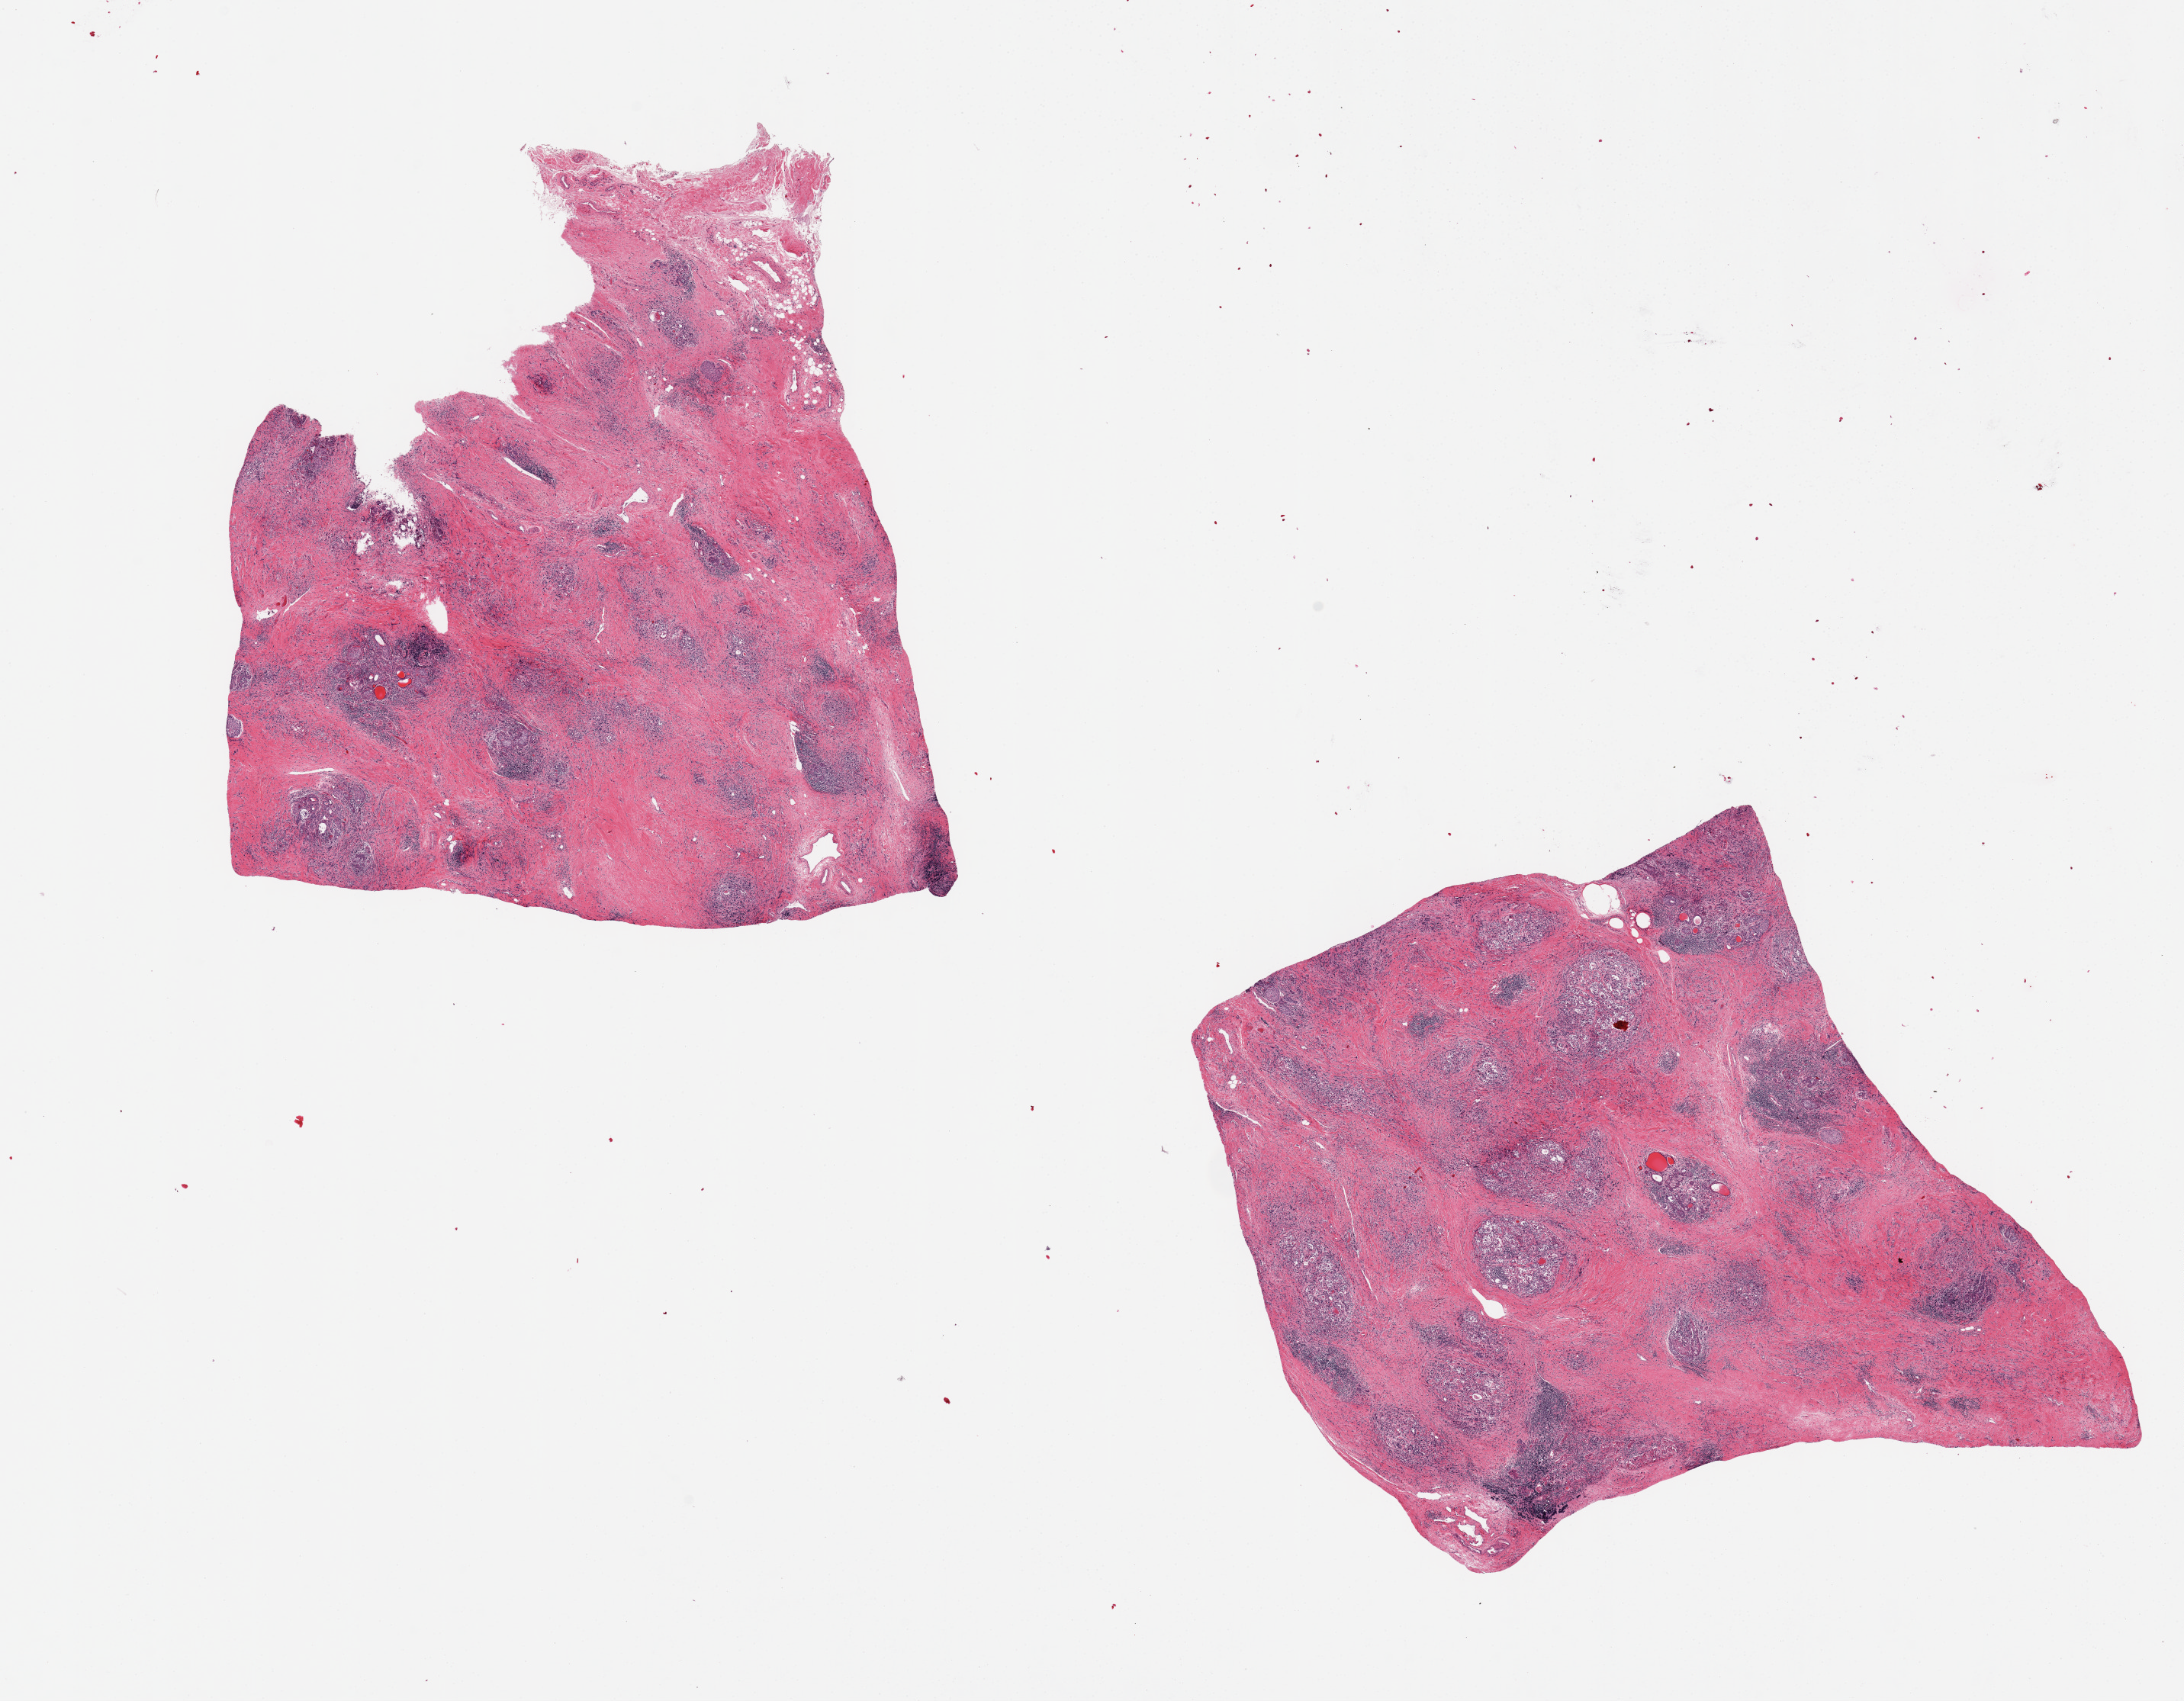
Digitized haematoxylin and eosin-stained section, whole scanned area (about 22.6 x 17.6 mm, from a 20x scan) shown as a low-resolution overview; PAXgene-fixed paraffin-embedded (PFPE) section; target tissue: thyroid; tissue donor sample.
Review note (as recorded): 2 pieces. Severe fibrosis and lymphoid infiltrate with minimal thyroid tissue remaining; foci of squamous metaplasia. Most likely Riedel's thyroiditis; but cannot exclude Hashimoto's.